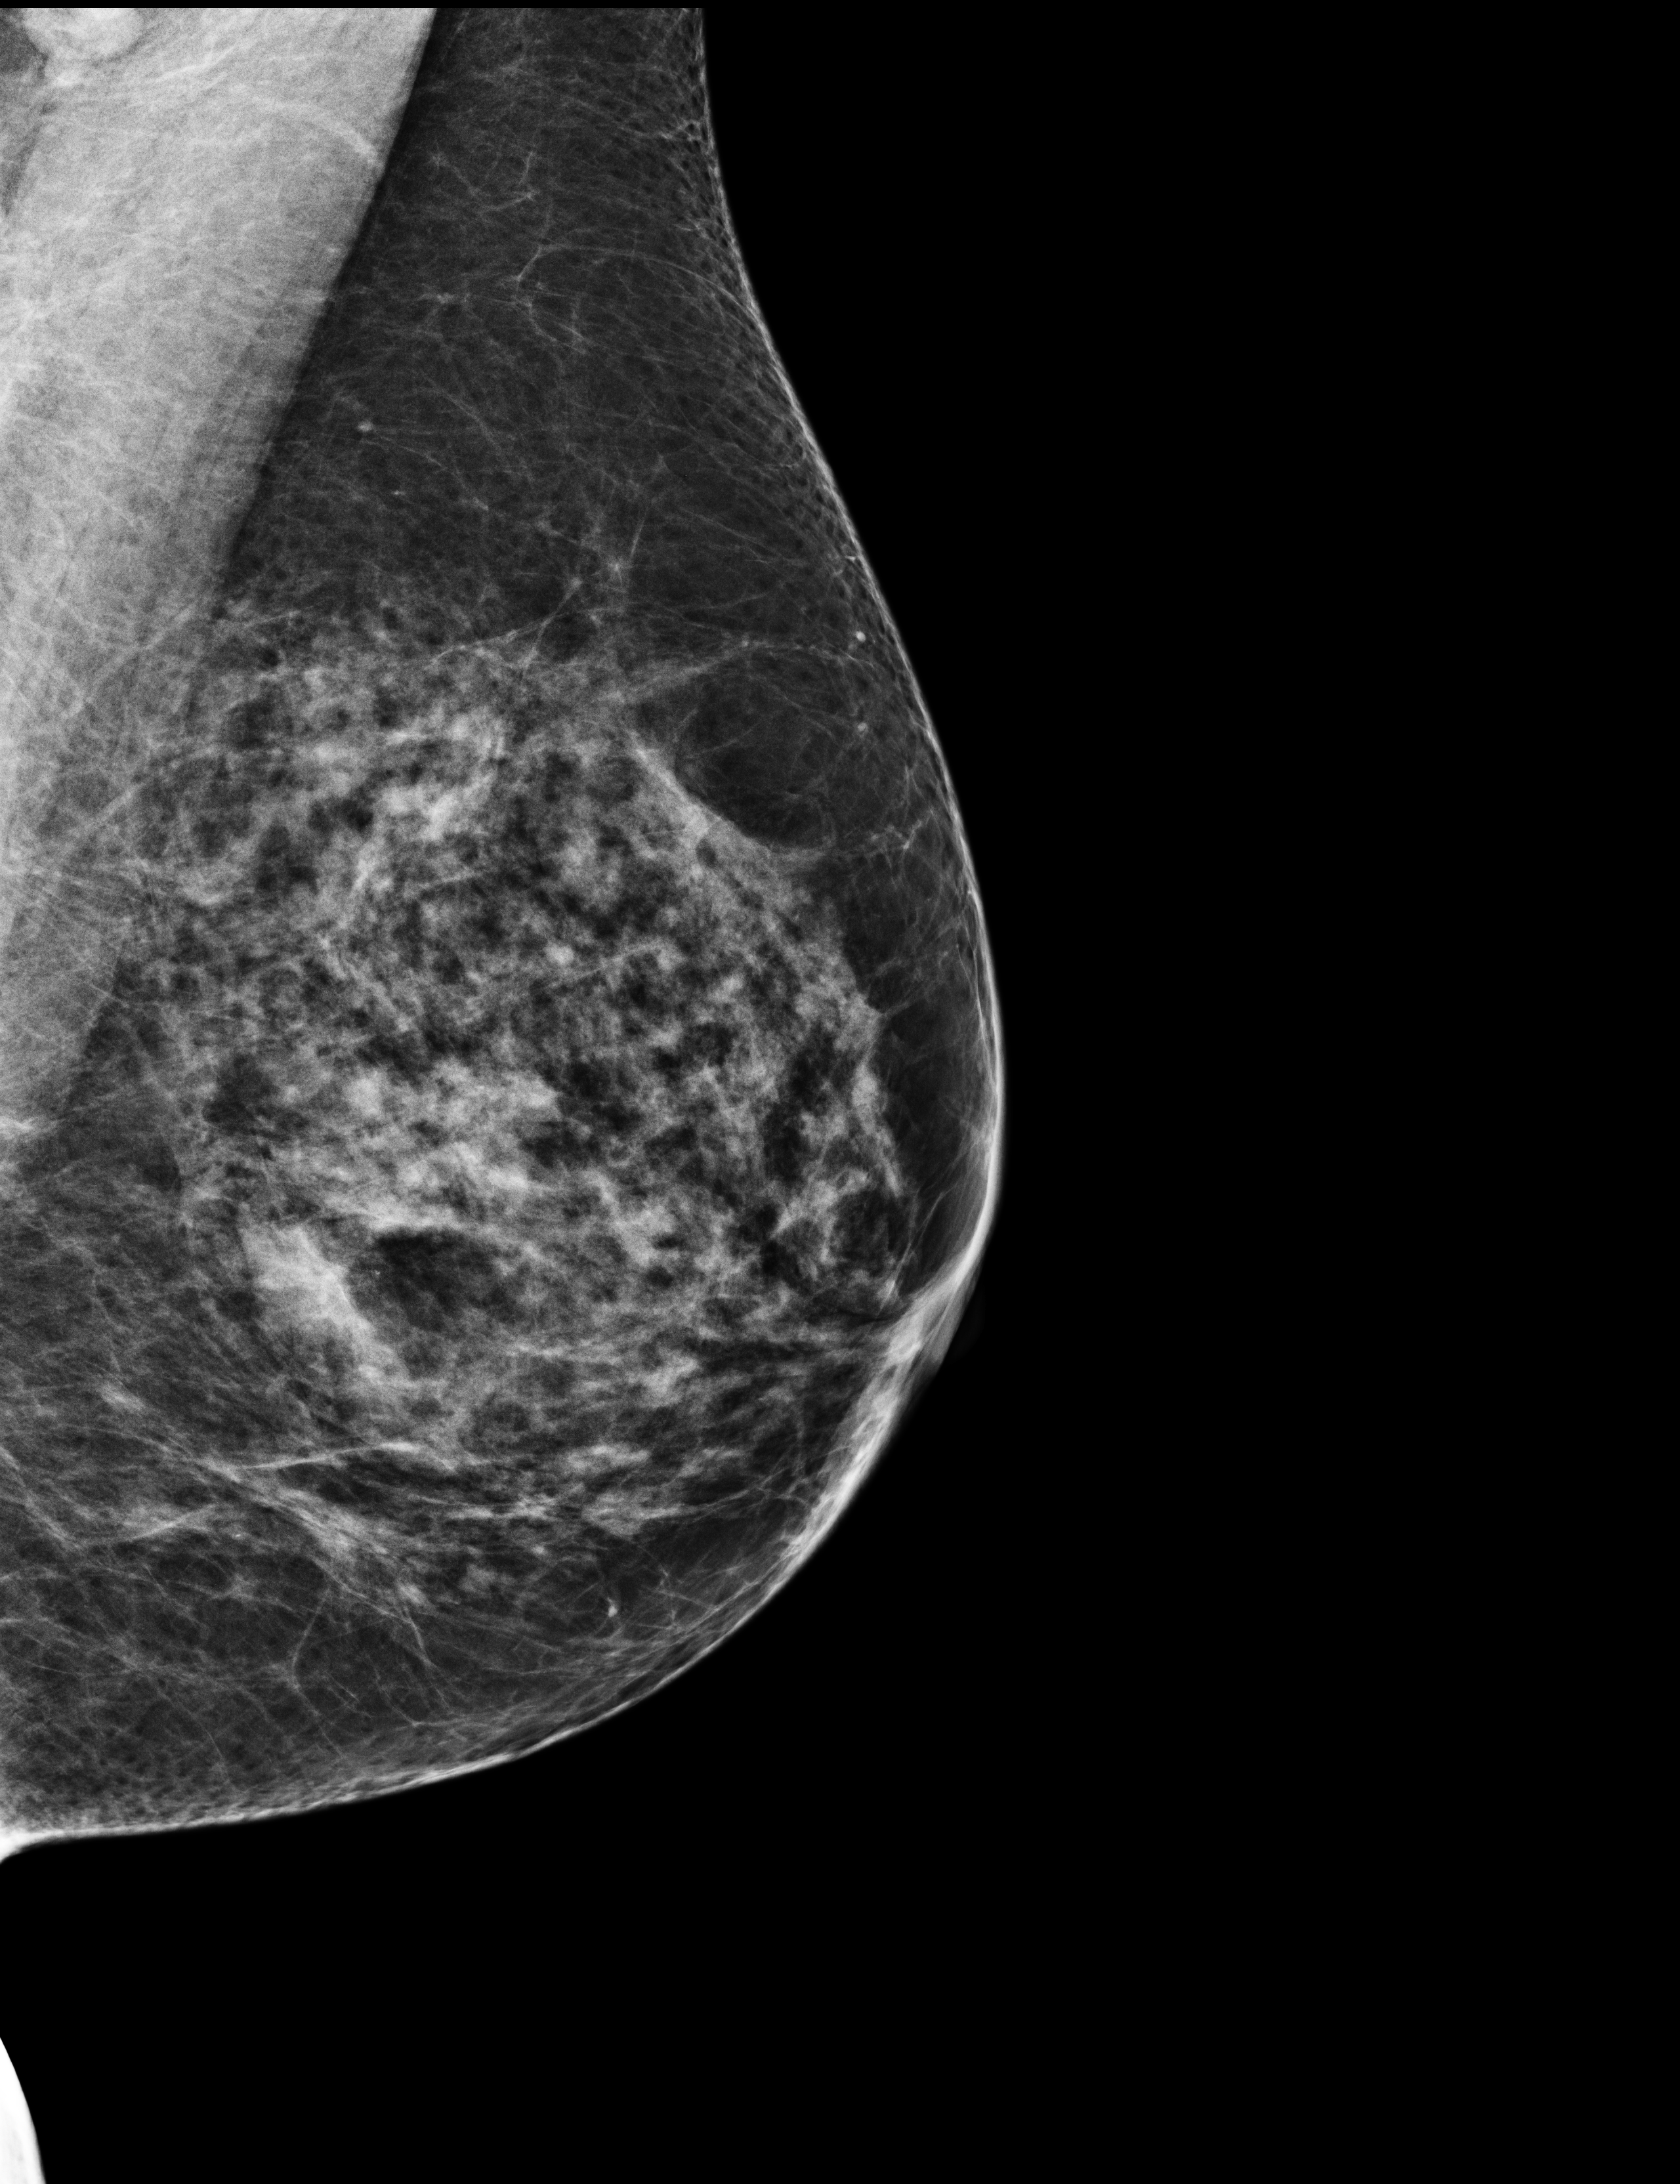
Digital mammogram (FFDM); left breast; MLO view; annual screening mammography examination; compressed breast thickness 61 mm. Patient aged 60 years (female).
Final BI-RADS category for the screening round (tomosynthesis exam, both breasts): category 1.